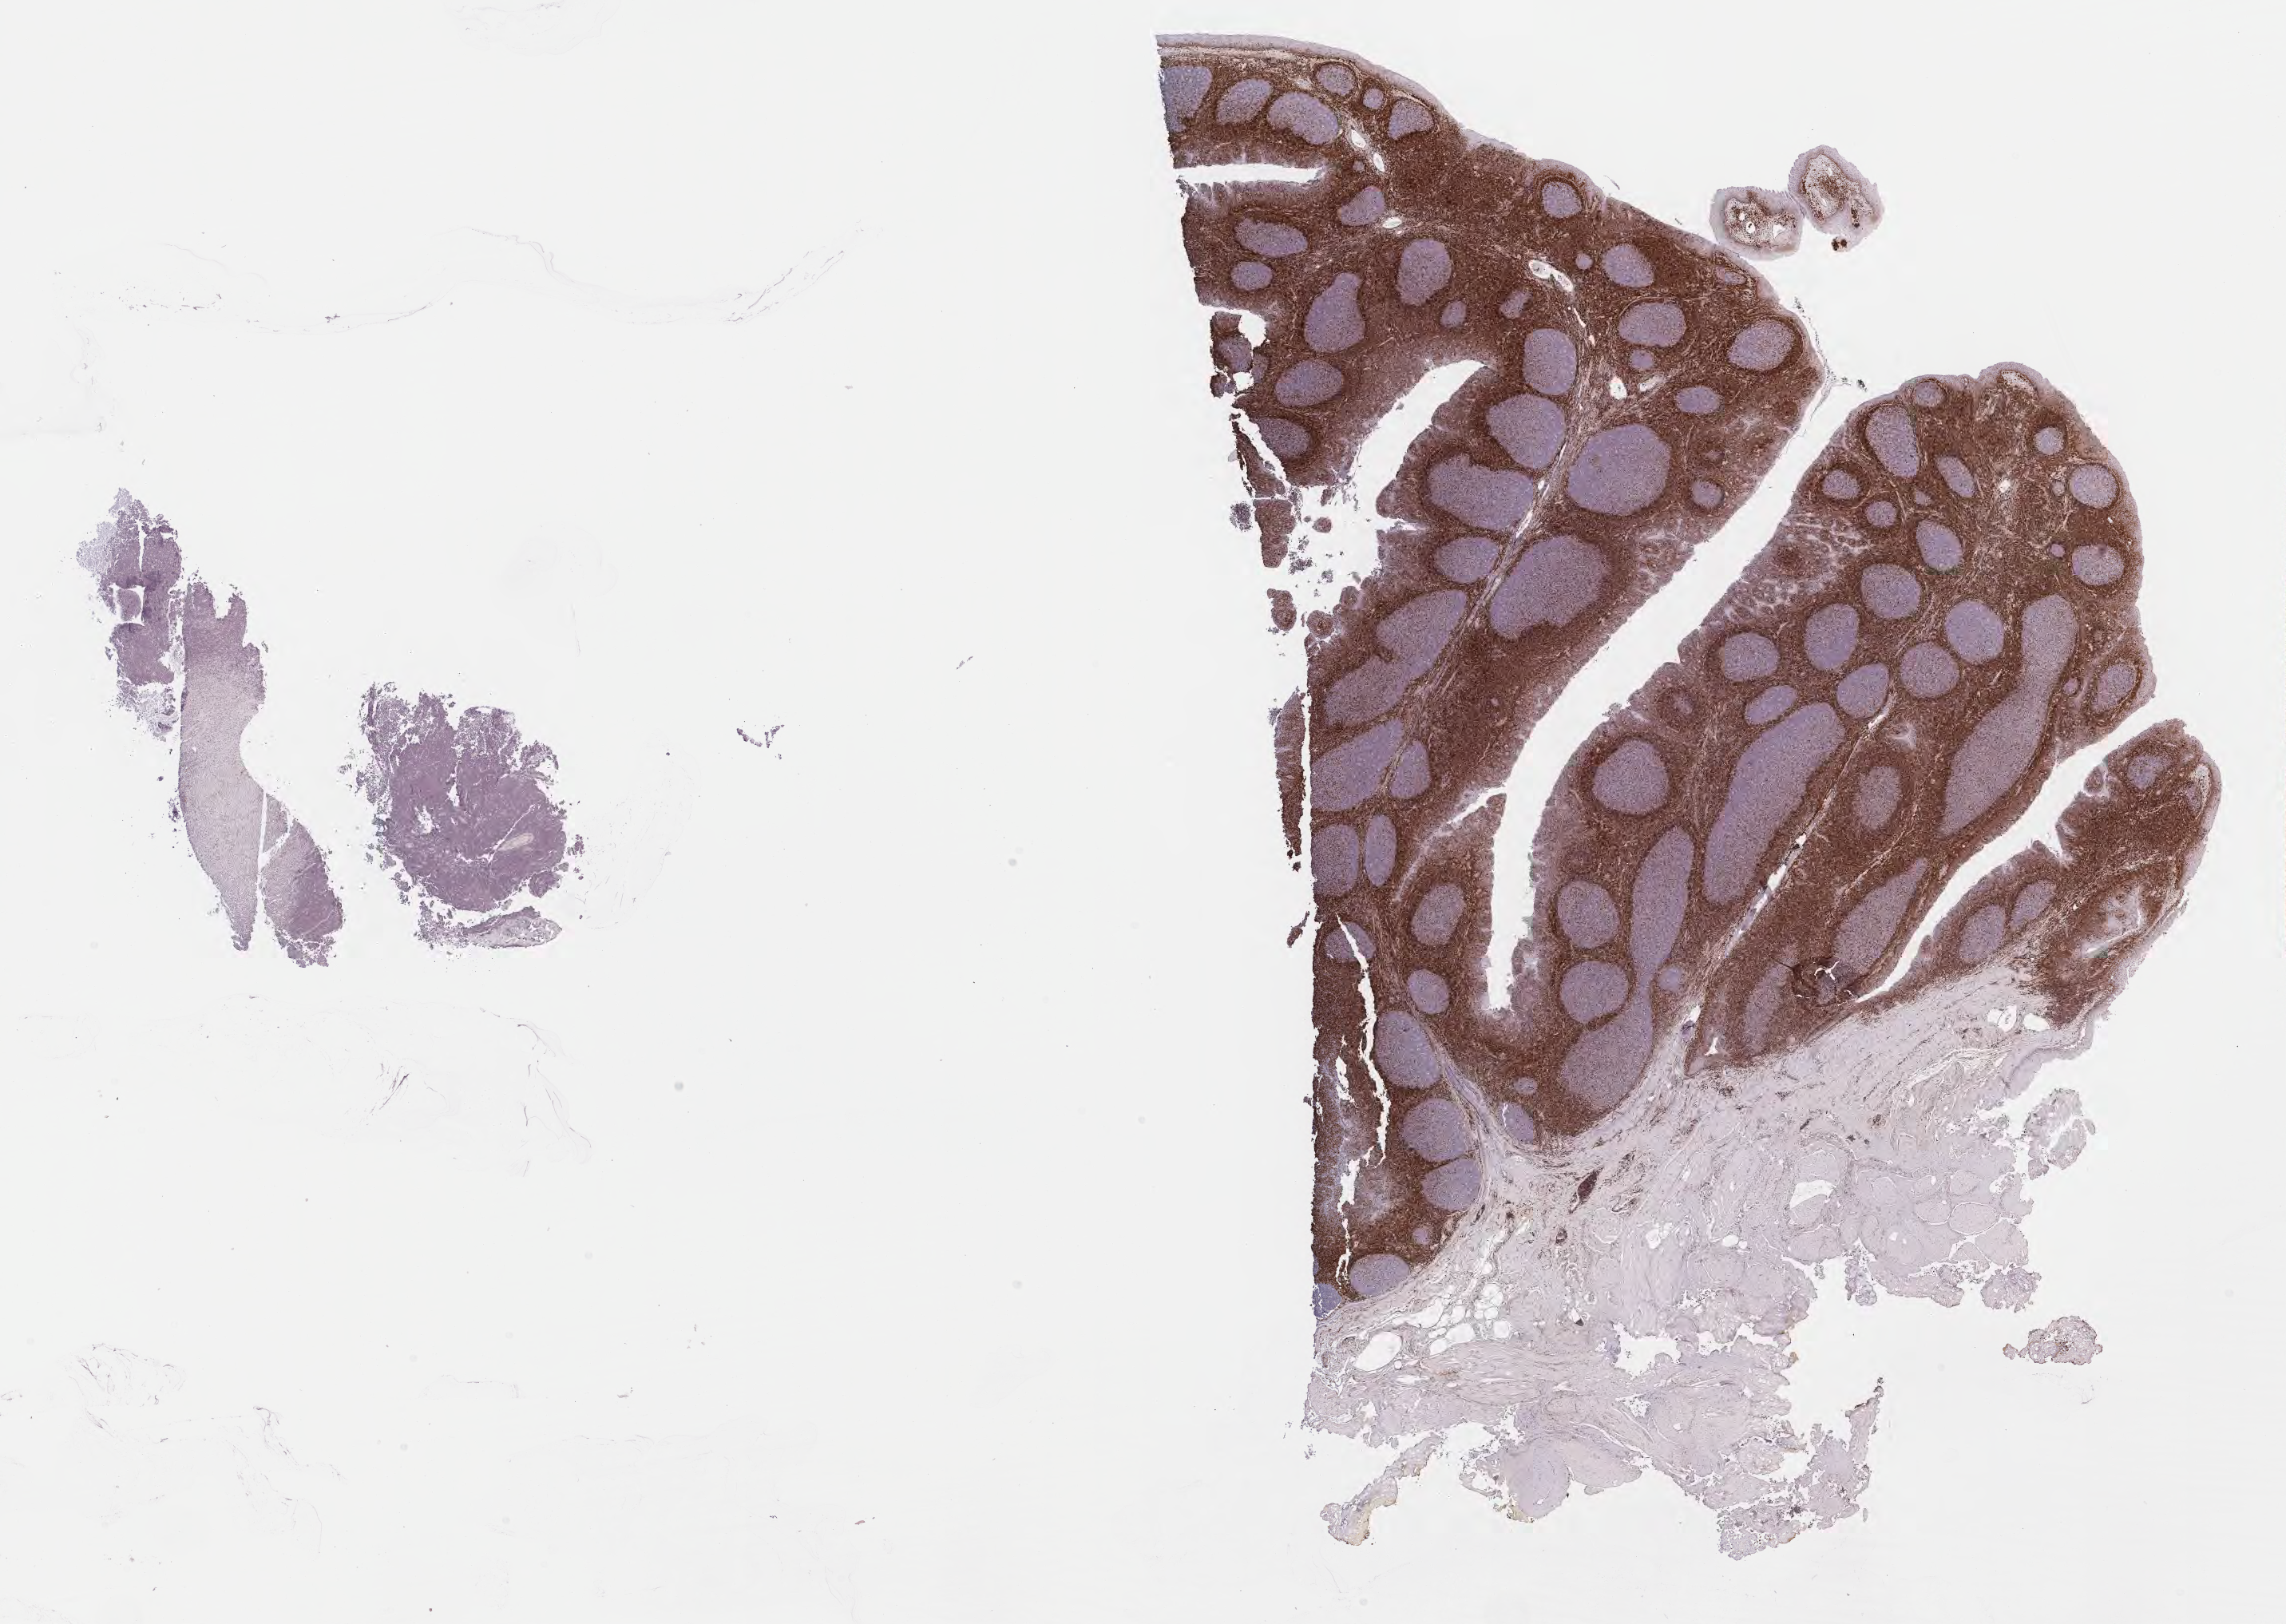
Whole-slide image, immunohistochemical stain for BCL2 — low-resolution overview of the scanned area, about 23.2 x 16.5 mm. Tumor tissue. Site: cranium. Male, age 4 years at initial diagnosis.
Histologic diagnosis: Burkitt lymphoma, NOS.